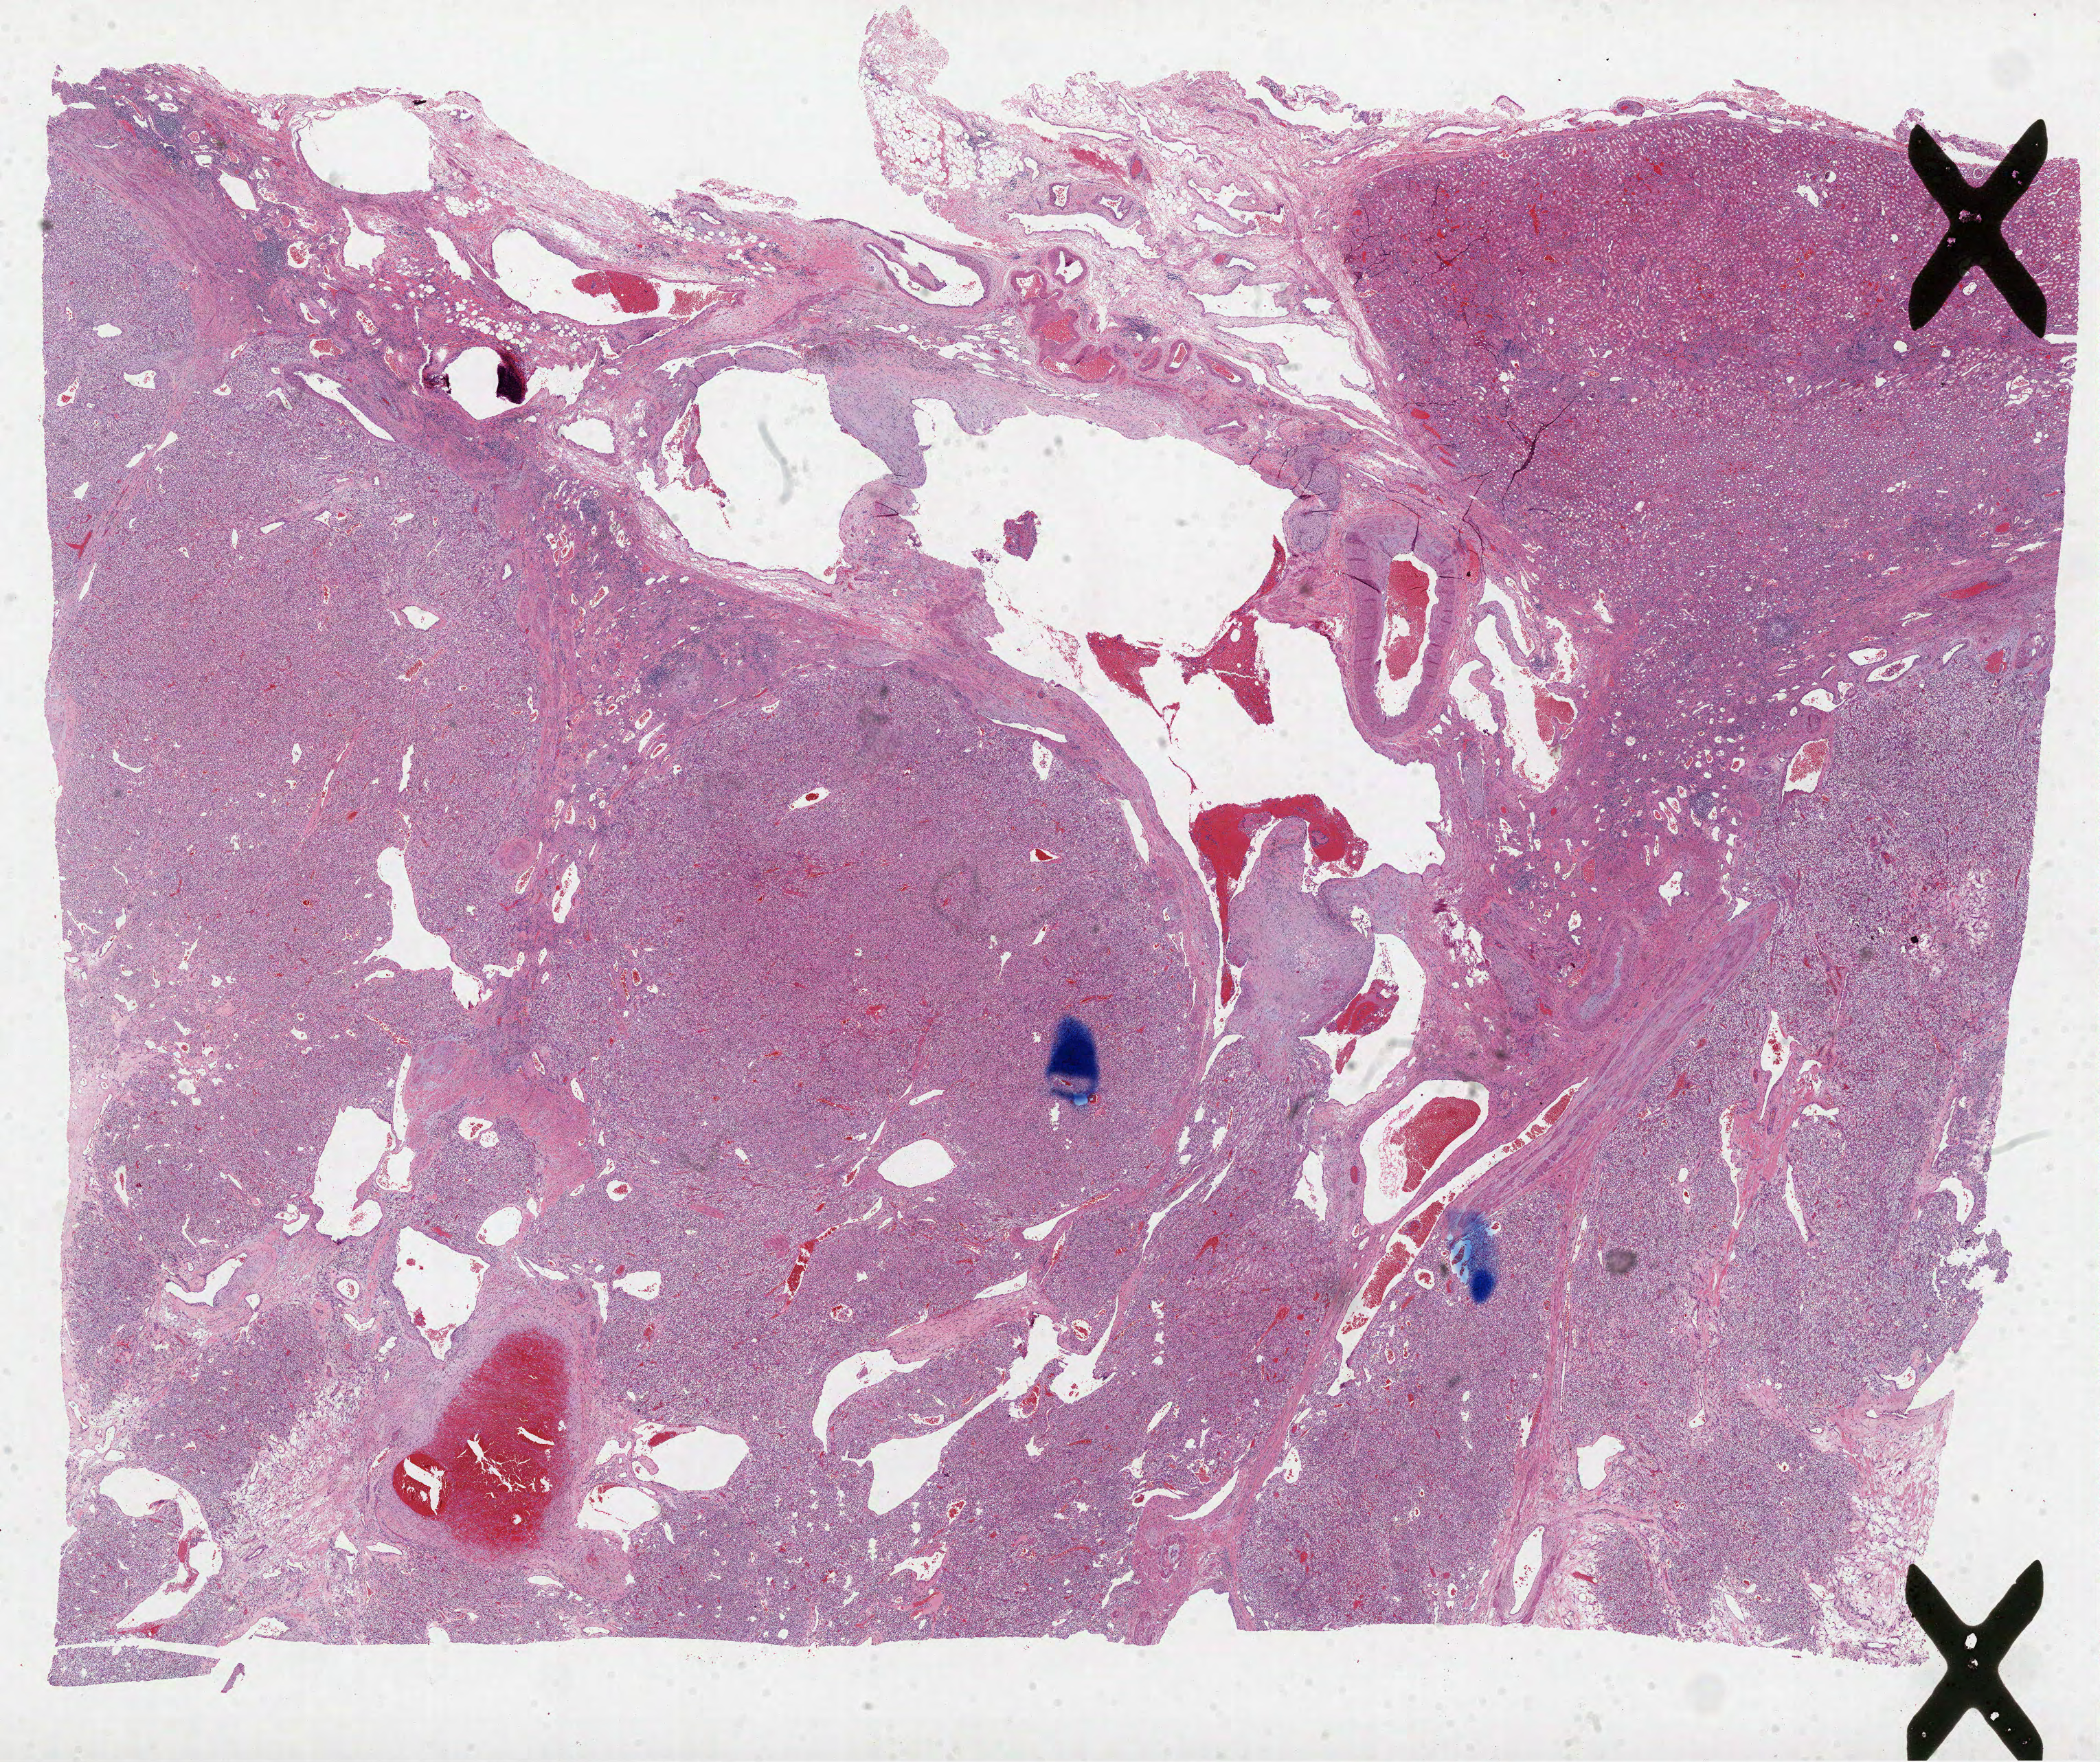
Whole-slide histology image, Hematoxylin and eosin (H&E) stained — low-resolution overview of the scanned area, about 24.7 x 20.7 mm (slide scanned at 40x); FFPE section; primary tumour sample from the kidney. Male, age 51 years at initial diagnosis. Histologic grade: G3 (poorly differentiated).
Histologic diagnosis: Clear cell adenocarcinoma, NOS. Laterality: left. AJCC pathologic stage: III.